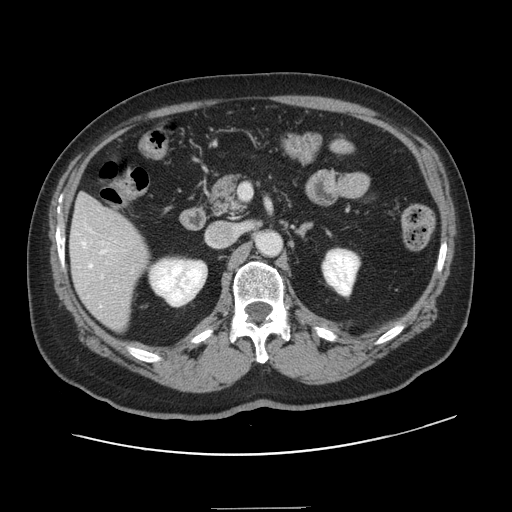
Contrast-enhanced abdominal CT, one axial slice. Position 68 of 143 along the scan axis. 120 kVp. Intravenous contrast given. Soft-tissue window (W 400 / L 40 HU). 512 × 512 image matrix, field of view 402 × 402 mm. Male patient, age 62 years. Case-level facts recorded for this patient, not image findings: diagnosis: colorectal cancer liver metastases, imaged before liver resection.
Annotated regions visible in this slice (manually delineated by an expert):
- hepatic veins: bounding box (x1, y1, x2, y2) in pixels: (81, 242, 106, 306)
- liver: (71, 195, 149, 330)
- planned liver remnant (the part of the liver to remain after resection): (75, 196, 105, 217)
- portal vein (with intrahepatic branches): (102, 242, 108, 264)